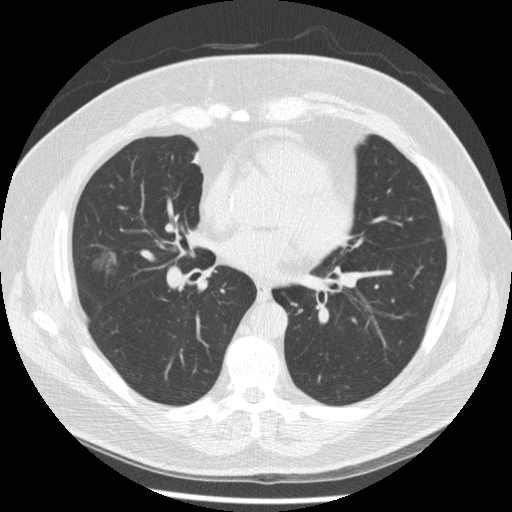
Low-dose screening chest CT, axial slice. Second screening round (one year after baseline). Lung window (W 1500 / L -600 HU). 2.5 mm slice thickness. 512 × 512 image matrix. Male participant, aged 67 years at enrolment.
- Expert-annotated lung lesion, box from (x=77, y=244) to (x=125, y=287) px.
- Screening reader's record for this exam (one nodule recorded; not confirmed to be the boxed lesion): non-calcified nodule or mass ≥4 mm, right middle lobe, 19 × 16 mm, smooth margins, soft tissue attenuation, pre-existing on the prior screen: yes; interval growth: yes.
- Lung cancer was diagnosed 47 days after this screen: adenocarcinoma, NOS, right middle lobe, moderately differentiated (G2), stage IA (AJCC 6th edition), 14 mm at pathology.